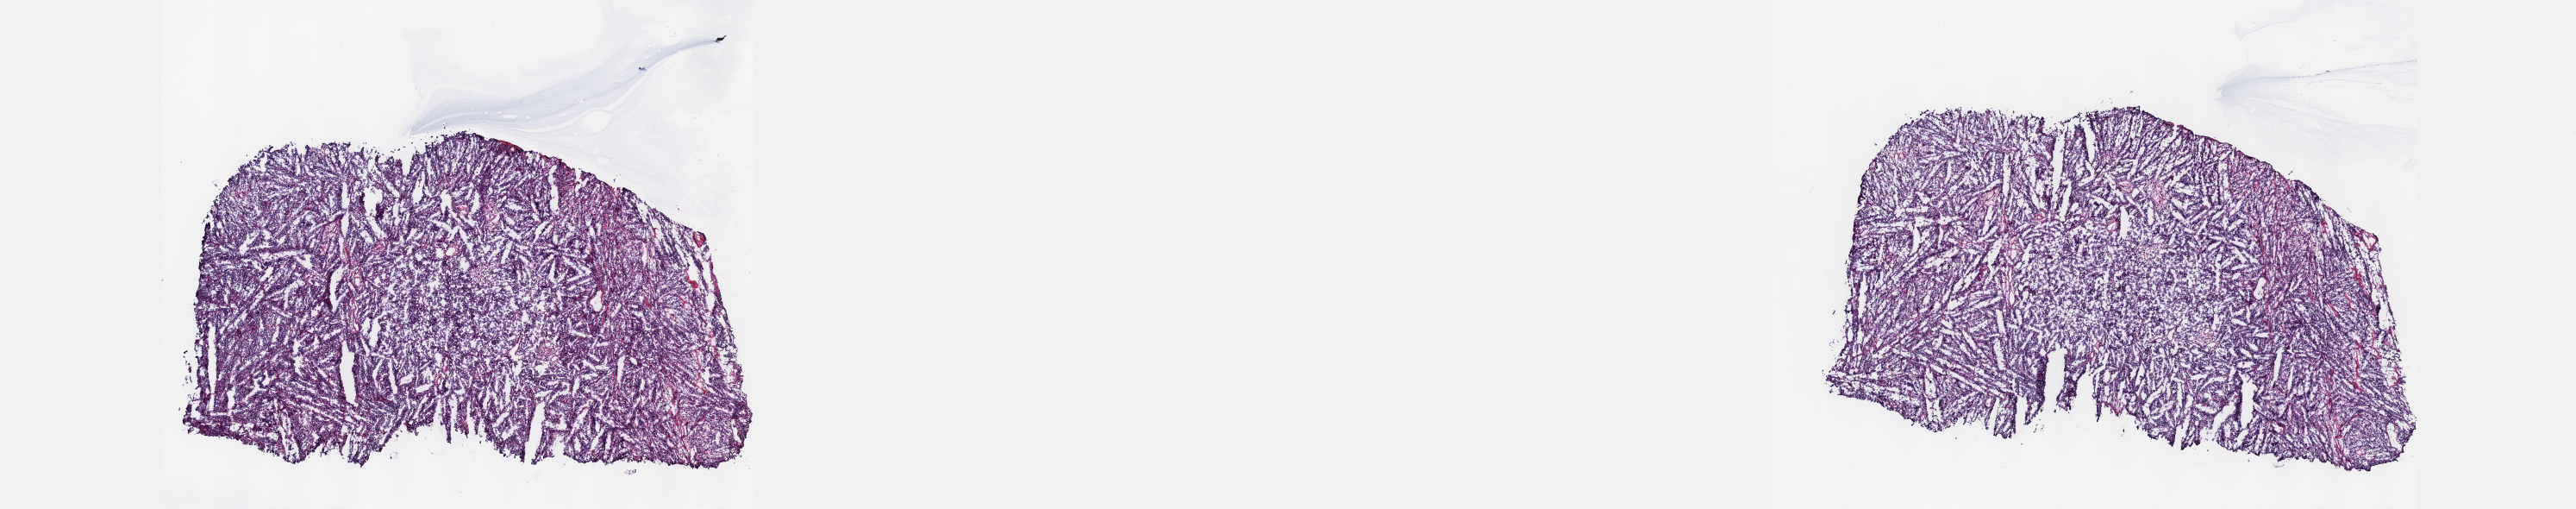
H&E-stained whole-slide image, low-resolution overview of the scanned area, about 24.1 x 4.8 mm (acquisition: 40x scan). Male patient. Pathologist review of this section (percent, as recorded): tumour cells 90%, tumour nuclei 90%.
Specimen: frozen section from the top of the tissue portion; sample: primary tumour, testis.